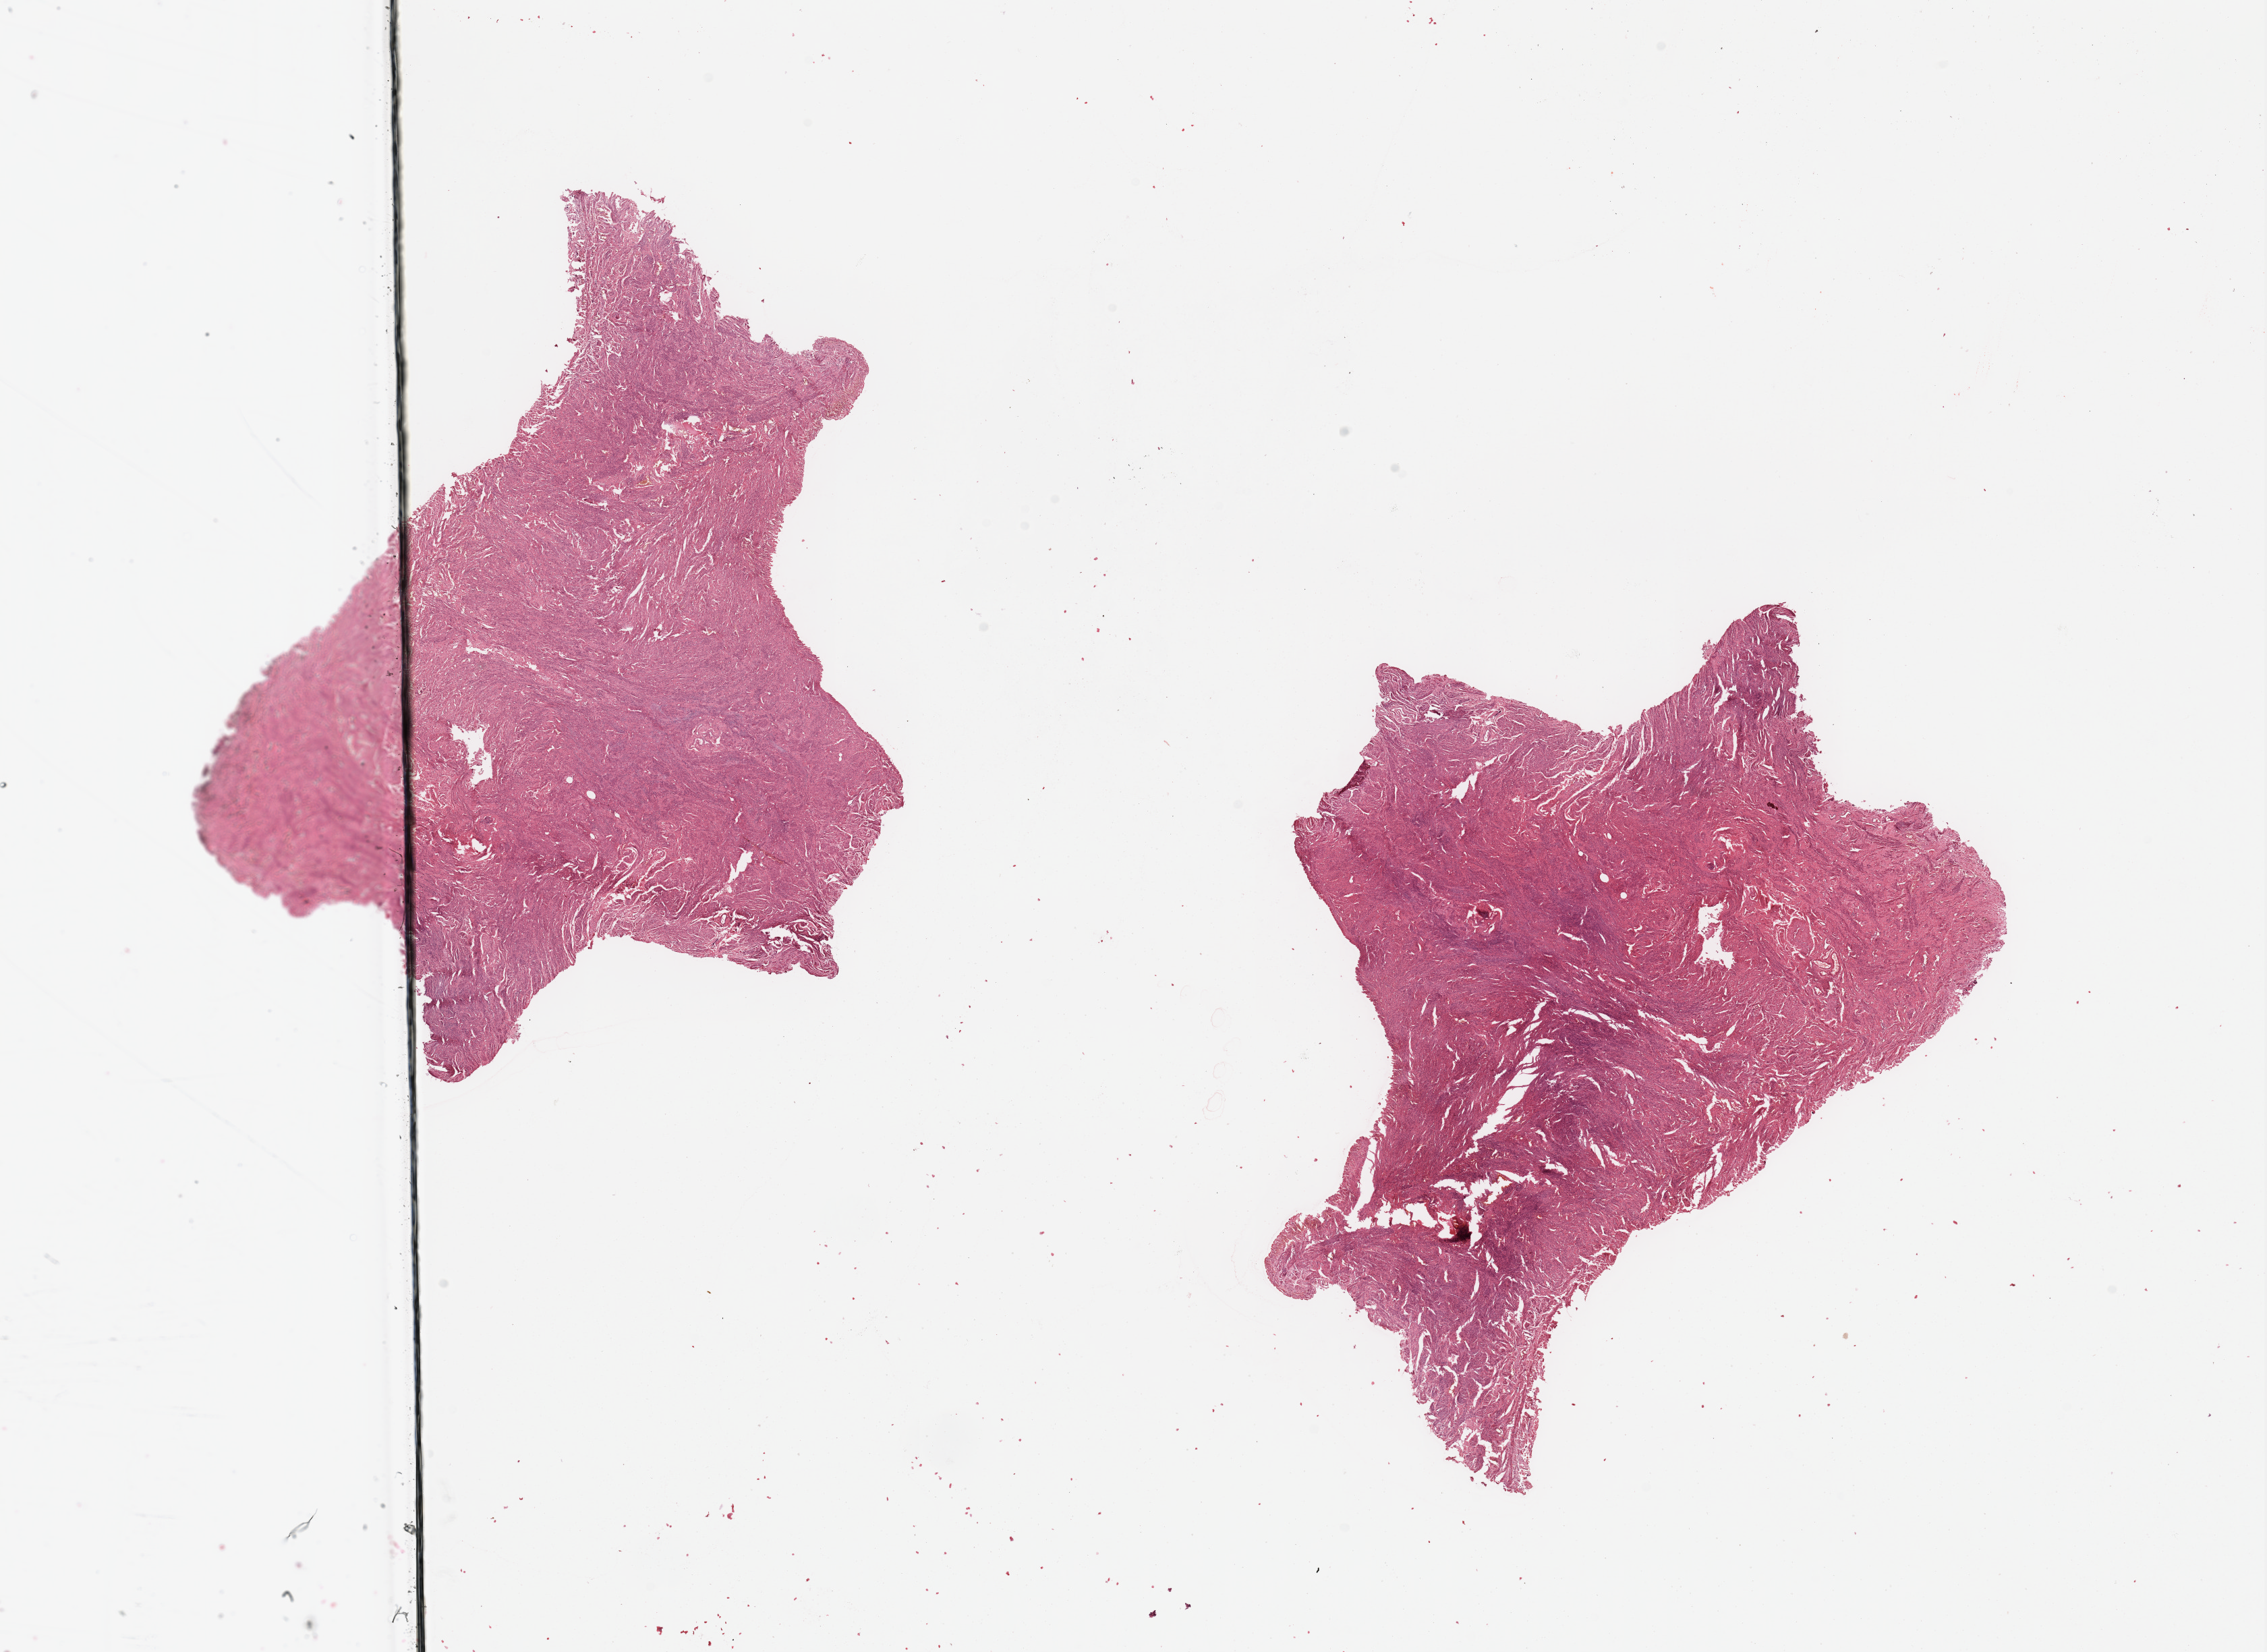
Whole-slide histology image, H&E-stained, a low-resolution overview of the entire scanned area, about 26.6 x 19.4 mm (acquisition: 20x scan). 80-year-old female patient.
Patient diagnosis (cohort enrolment): sarcoma (site not recorded at cohort level). Primary tumour site (as recorded): gynecologic.